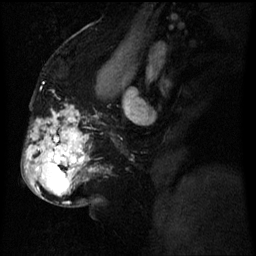
Breast MRI (dynamic contrast-enhanced), one sagittal slice. Slice 34 of 60 in the series (ordered by position). Dynamic contrast-enhanced series, image 2 of 3 at this slice position (ordered by acquisition). 1.5 T. TE 4.2 ms, TR 8 ms. 2.5 mm slice thickness. 256 × 256 image matrix. Patient: female, 50 years.
Annotated regions visible in this slice (semi-automatic segmentation, software-assisted and operator-edited):
- analysis volume of interest (the breast-tissue region the enhancement analysis was run in; not a lesion): bounding box (x1, y1, x2, y2) in pixels: (26, 112, 90, 199)
- tumour enhancement mask (voxels above the 70 % enhancement threshold inside the analysis volume of interest): (30, 132, 80, 175)